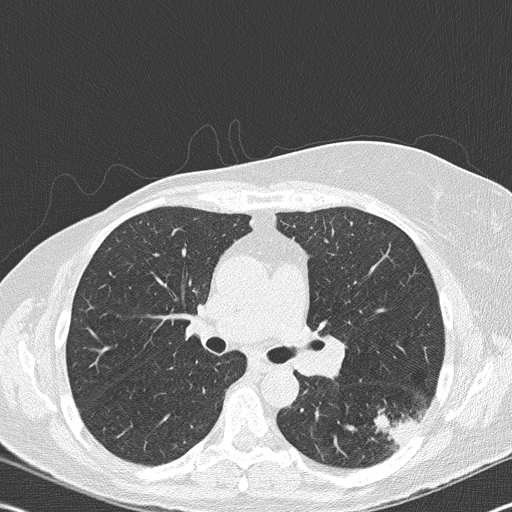
Low-dose screening chest CT, one axial slice. Position 109 of 177 along the scan axis. Reconstruction kernel B50f. Lung window (W 1500 / L -600 HU). 2 mm slice thickness. 512 × 512 image matrix, field of view 342 × 342 mm.
Annotated regions visible in this slice (outlined manually by an expert reader):
- lesion 1 (tumor): box from (x=375, y=414) to (x=420, y=447) px
- lesion 2 (nodule, hilum of left lung): (x=298, y=341)–(x=346, y=375)